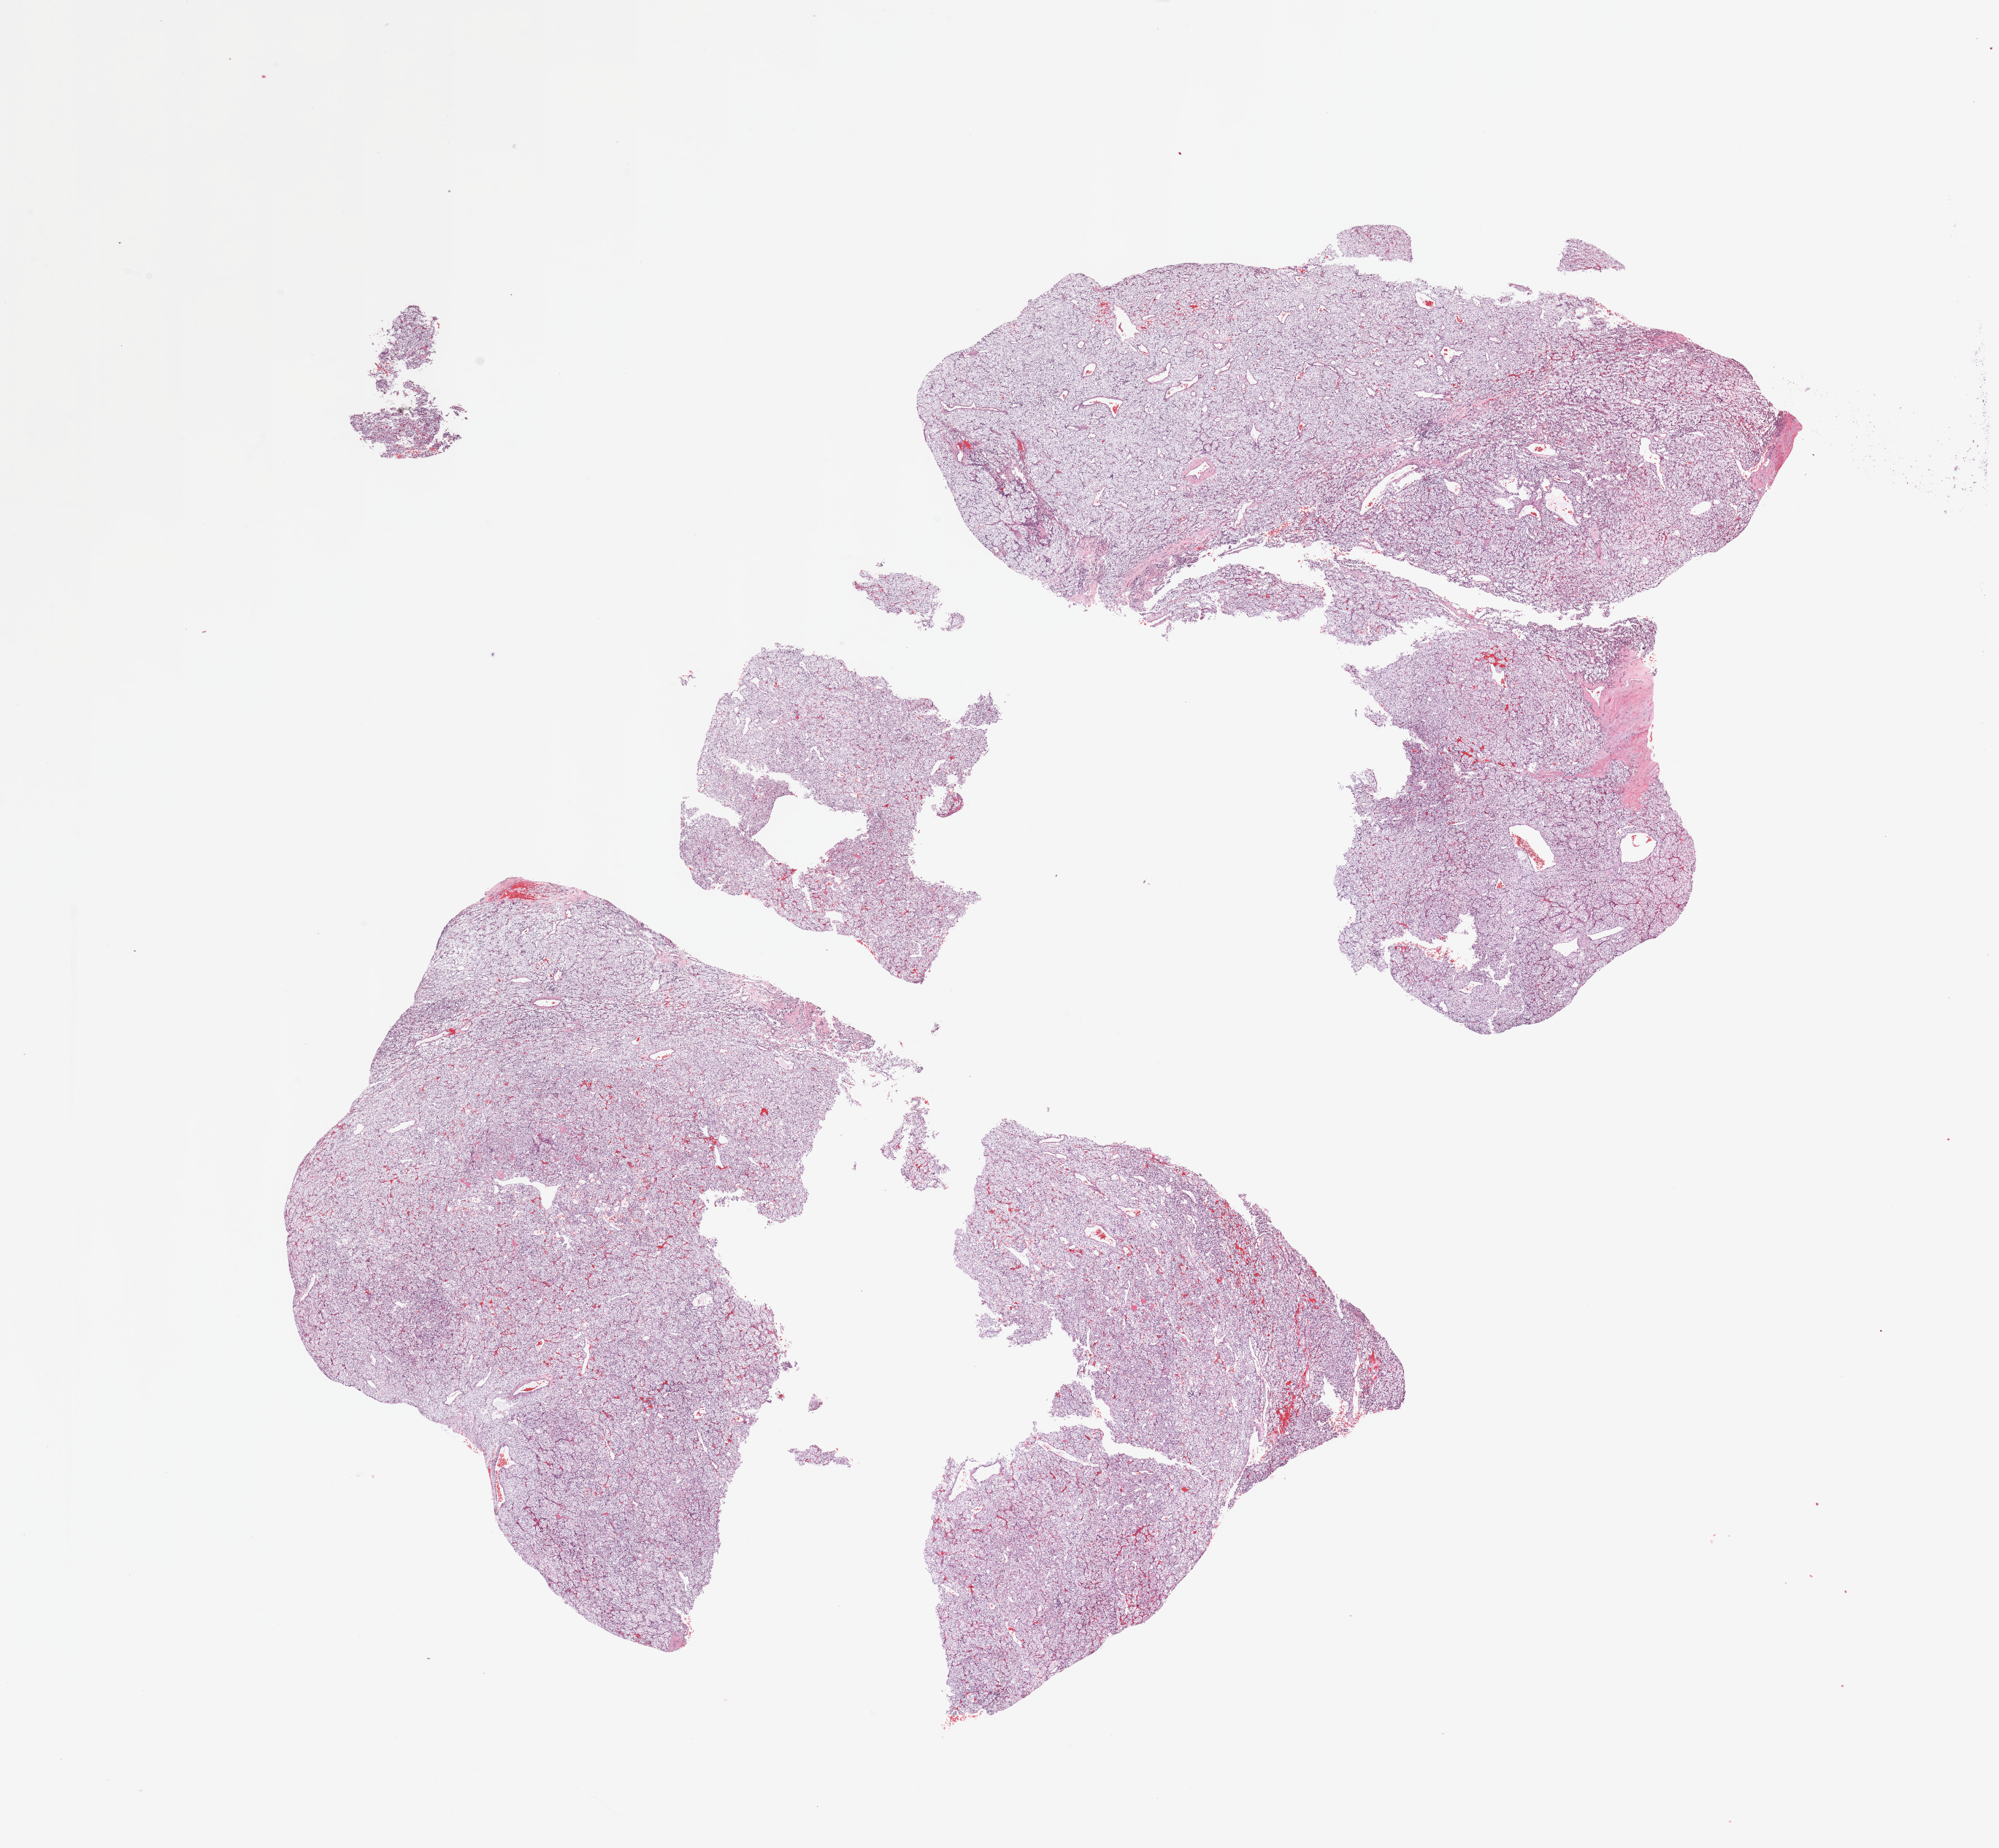
H&E-stained whole-slide image, whole scanned area (about 21.7 x 20.0 mm, acquisition: 20x scan) shown as a low-resolution overview; tumour tissue sample, sampled site: kidney. Male, 76 y/o. Histologic grade: G3 (poorly differentiated). Composition of this section per pathologist review: tumour nuclei 90%, necrosis 0%.
* diagnosis: Renal cell carcinoma, NOS
* AJCC pathologic stage: III